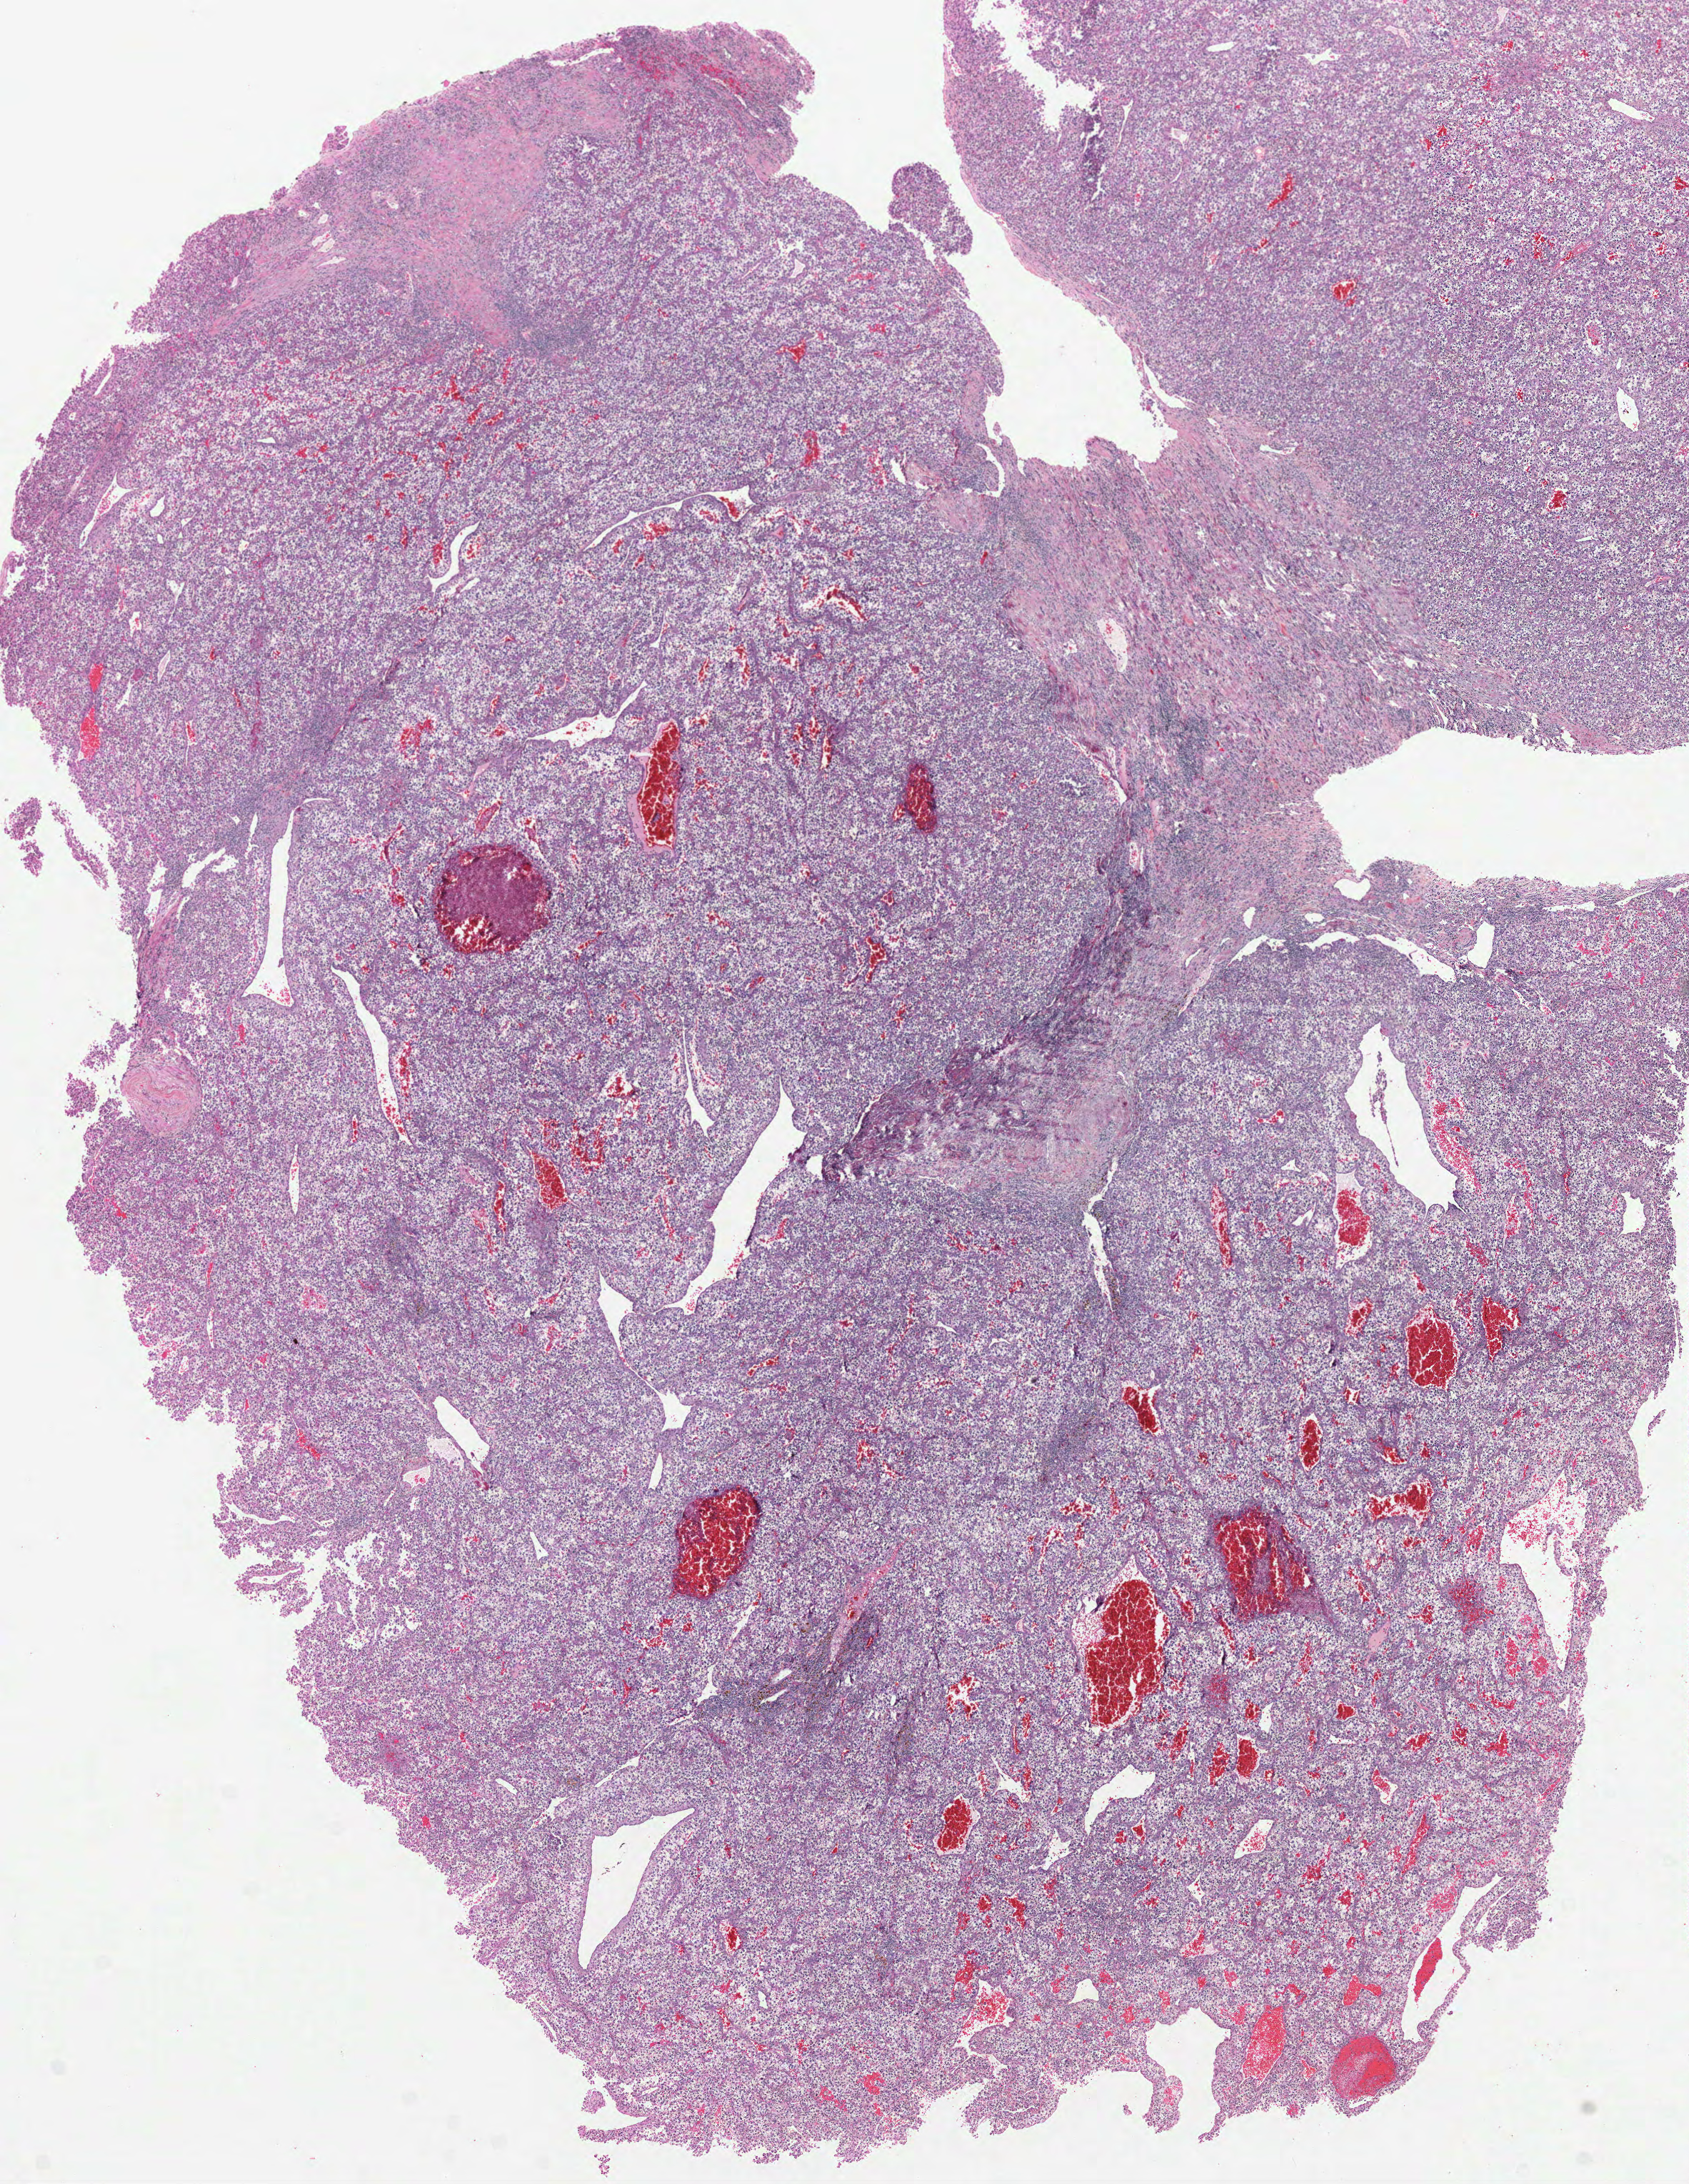
Hematoxylin and eosin (H&E) stained whole-slide image, shown as a low-resolution overview of the whole scanned area (about 9.5 x 12.3 mm, acquisition: 40x scan); FFPE section; primary tumour sample from the kidney. Patient: female, age at initial diagnosis 66 years. Histologic grade: G3 (poorly differentiated).
• lymph nodes positive (case pathology): 0 of 2 examined
• laterality: left
• diagnosis: Clear cell adenocarcinoma, NOS
• AJCC pathologic stage: IV